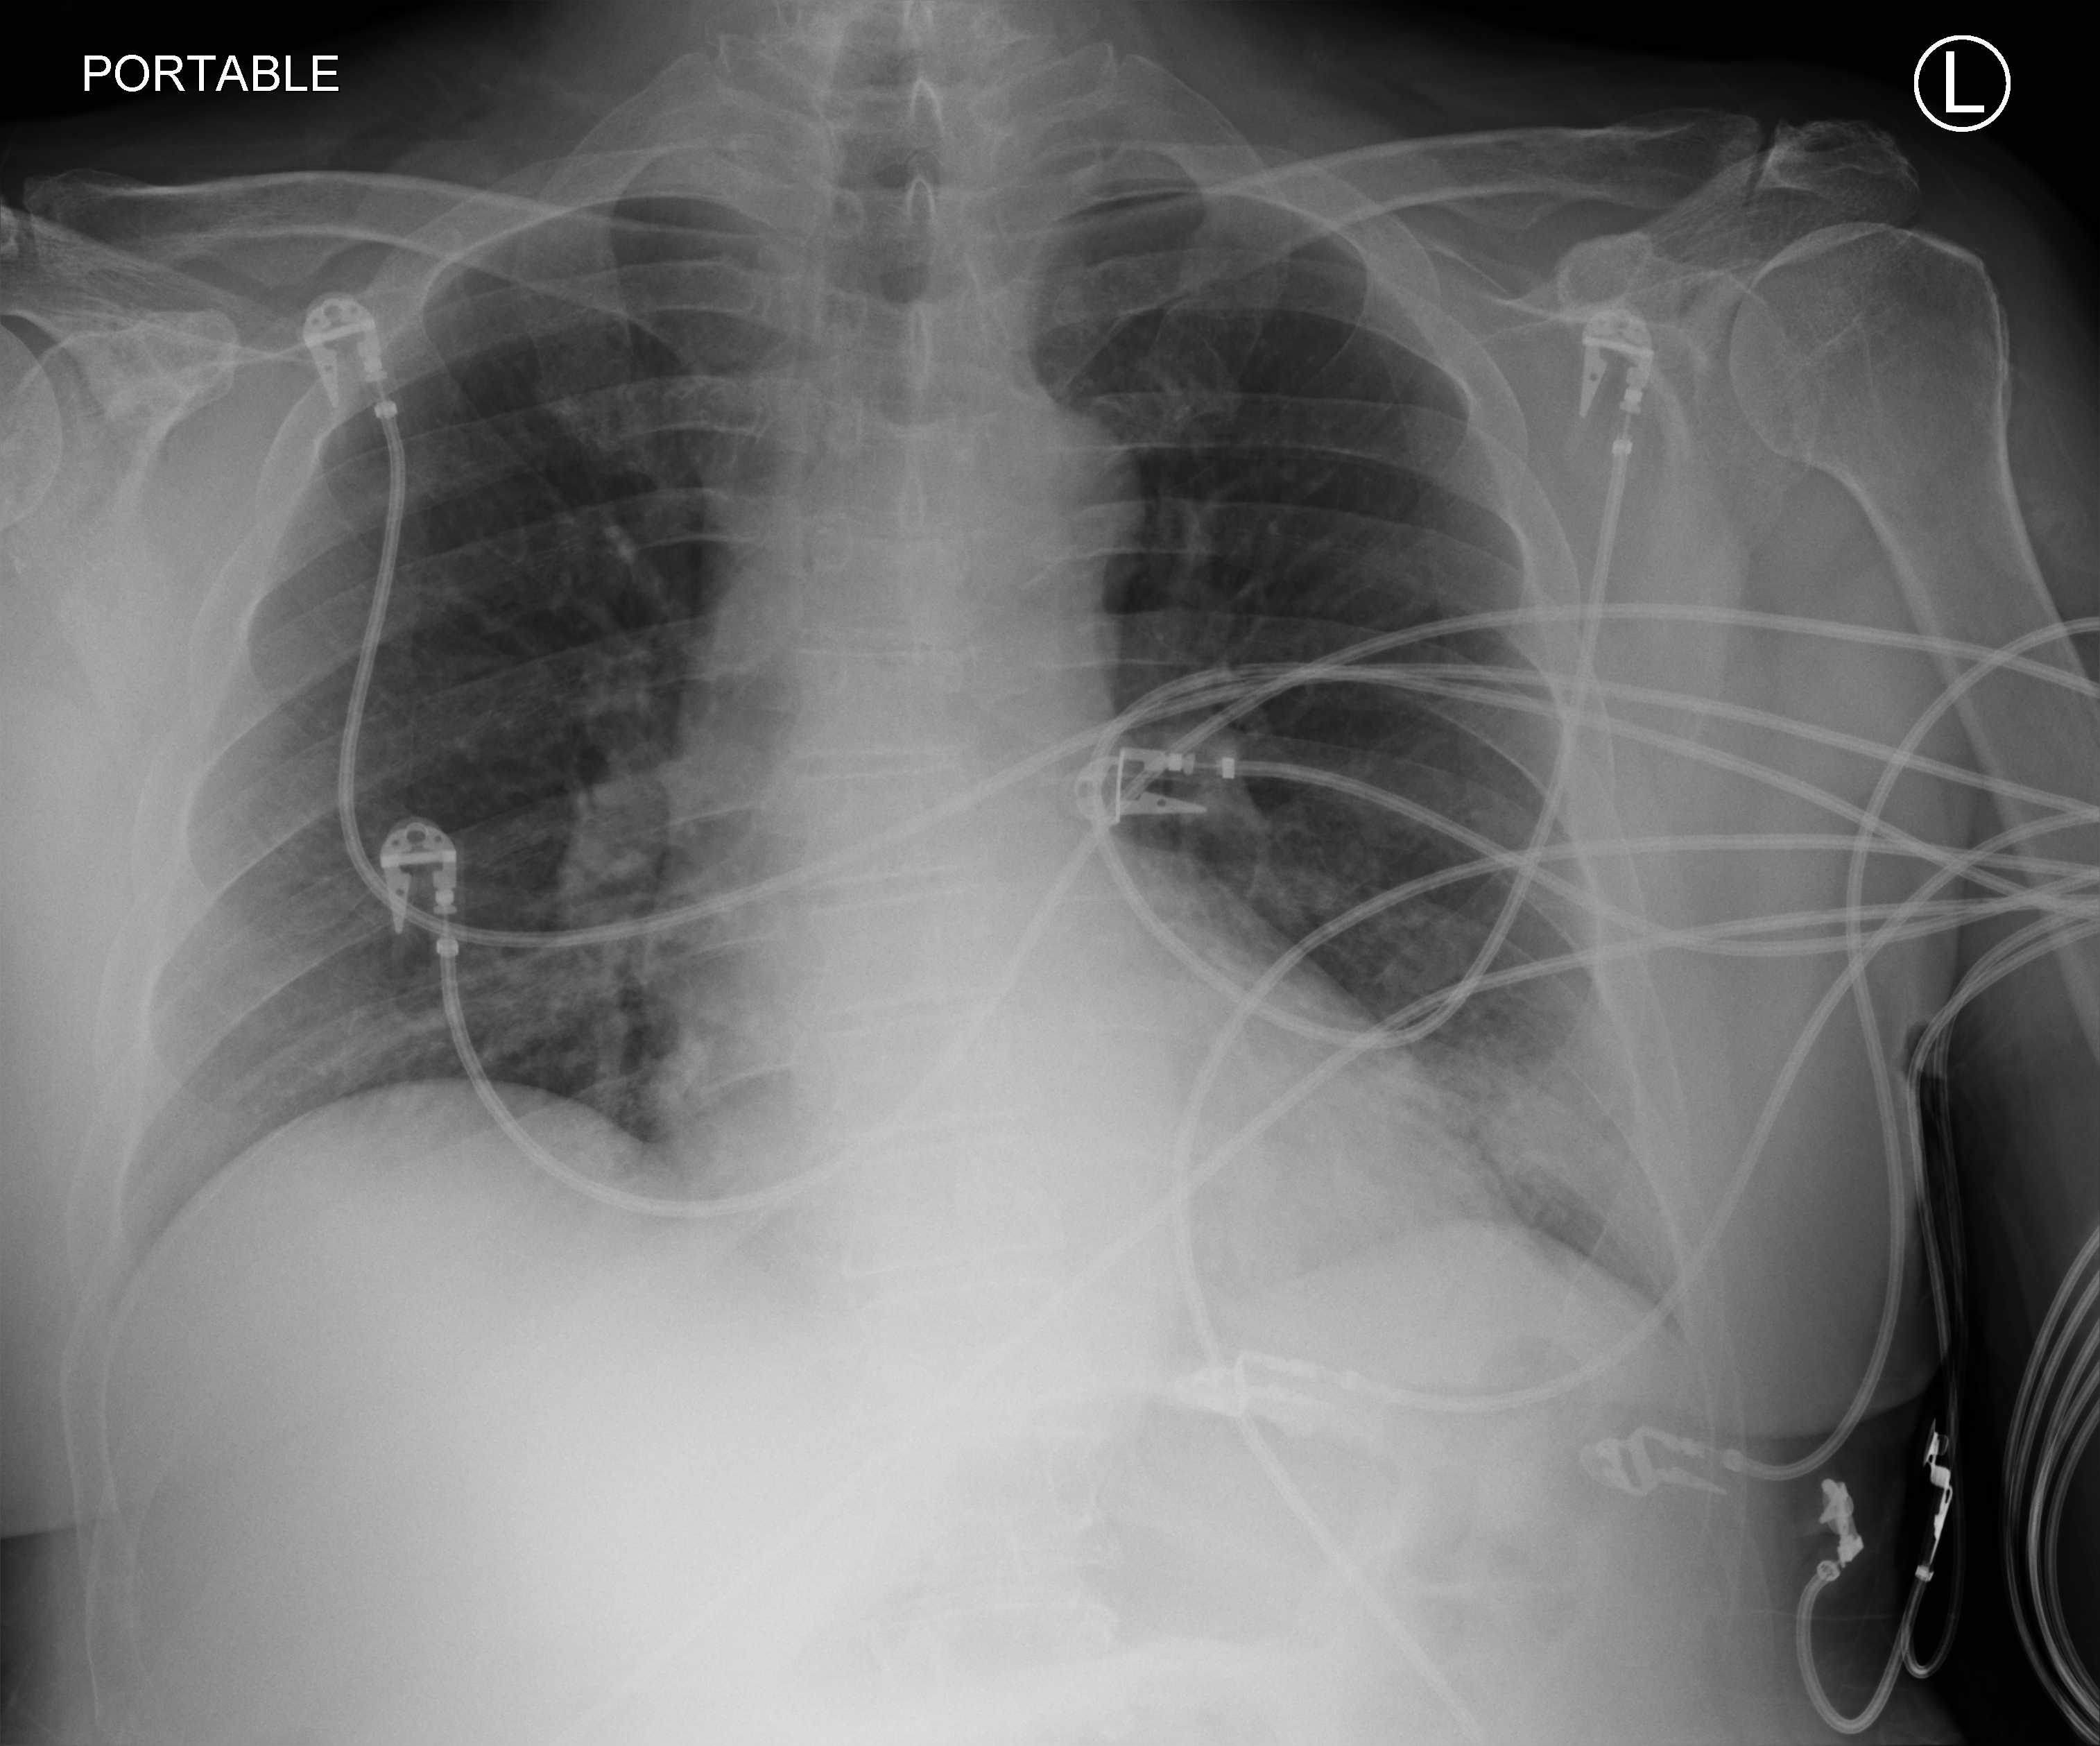
Portable chest radiograph; anteroposterior (AP) projection. Patient hospitalised with COVID-19; male, aged 60–74 years.
Admission-level facts for this patient (not findings on this image; timing relative to this image not recorded): smoking status (admission record): never; mechanically ventilated during this hospital stay: yes.